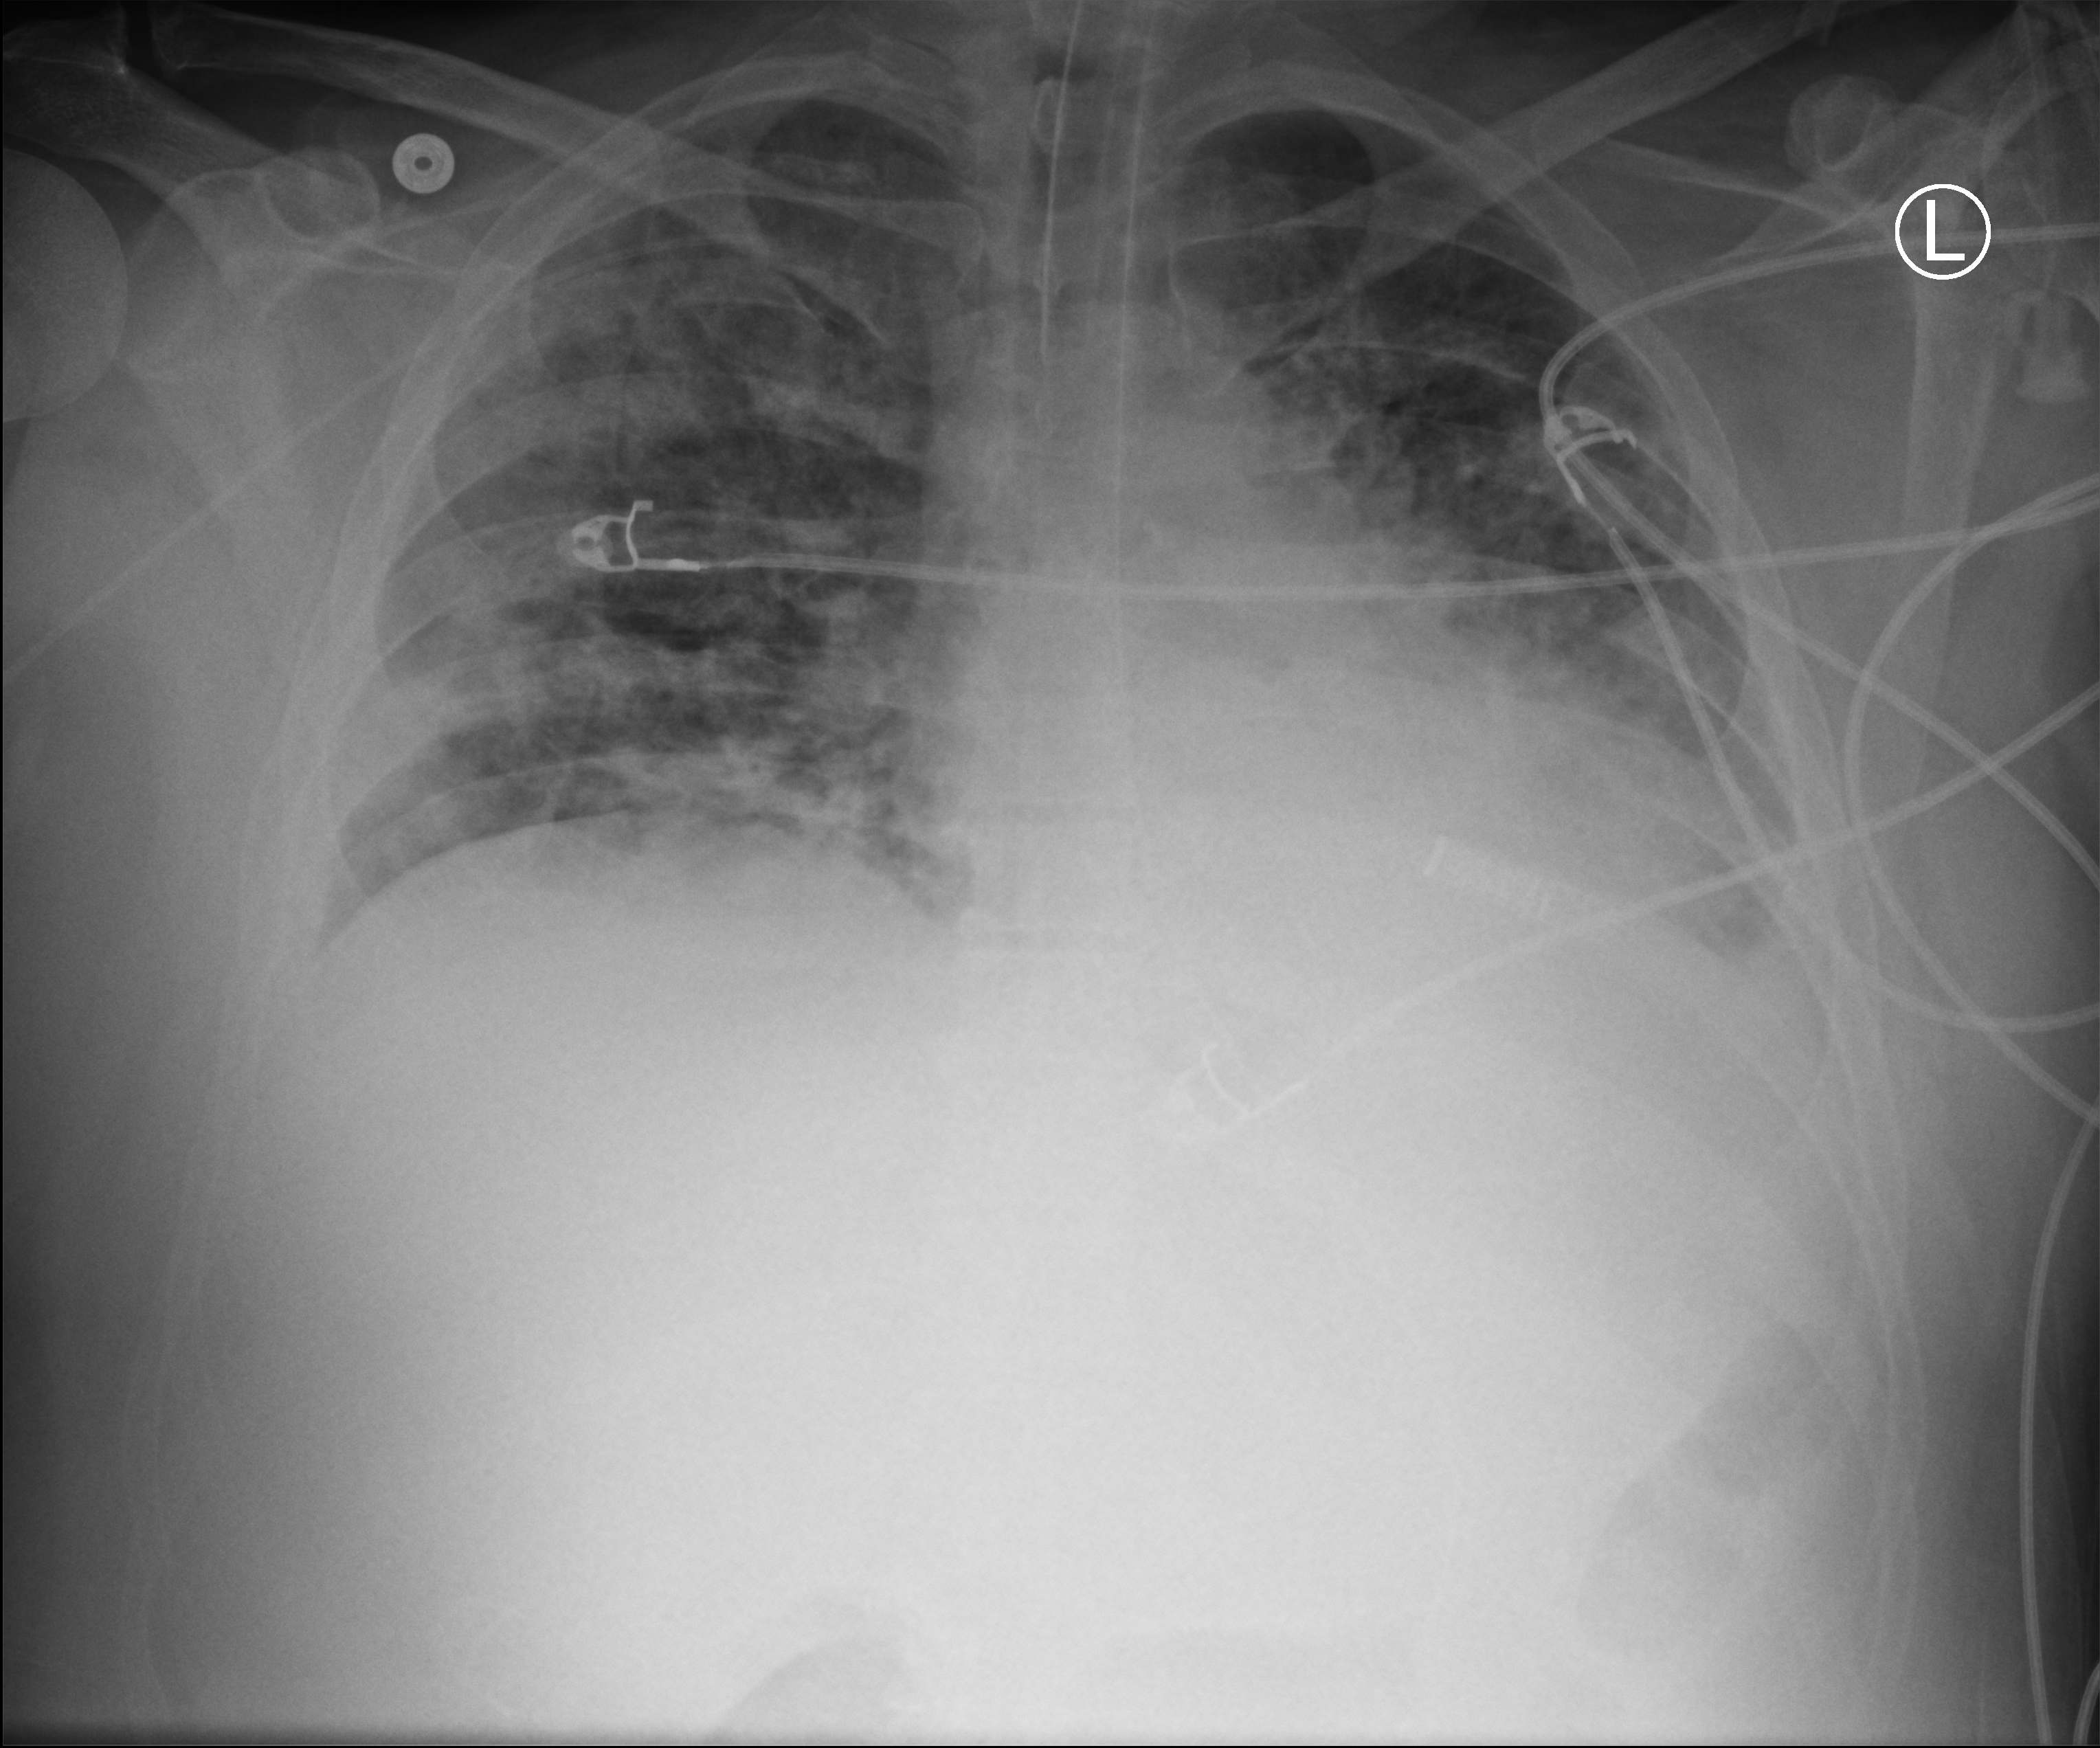
Bedside chest radiograph (computed radiography). Patient hospitalised with COVID-19; male, aged 18–59 years.
Hospital-stay facts (about this admission, not read from this image; timing relative to this image not recorded):
- hypertension (admission record): yes
- COPD (admission record): no
- admitted to intensive care during this hospital stay: yes